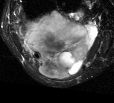
MRI of an extremity soft-tissue mass, one axial slice. Slice 22 of 44 in the series (ordered by position). T2-weighted fat-saturated. MR volume resampled by the dataset authors to the PET/CT grid (not the native acquisition matrix). 3.27 mm slice thickness. 114 × 103 image matrix, field of view 111 × 101 mm. Female patient. From the clinical record (not read from this slice): histological type: liposarcoma; site of the primary tumour: right thigh.
Outlined on this slice (expert contour drawn on MRI and transferred to this co-registered scan by the dataset authors):
- gross tumour volume (mass): bounding box [x1, y1, x2, y2] px = [20, 10, 101, 78]